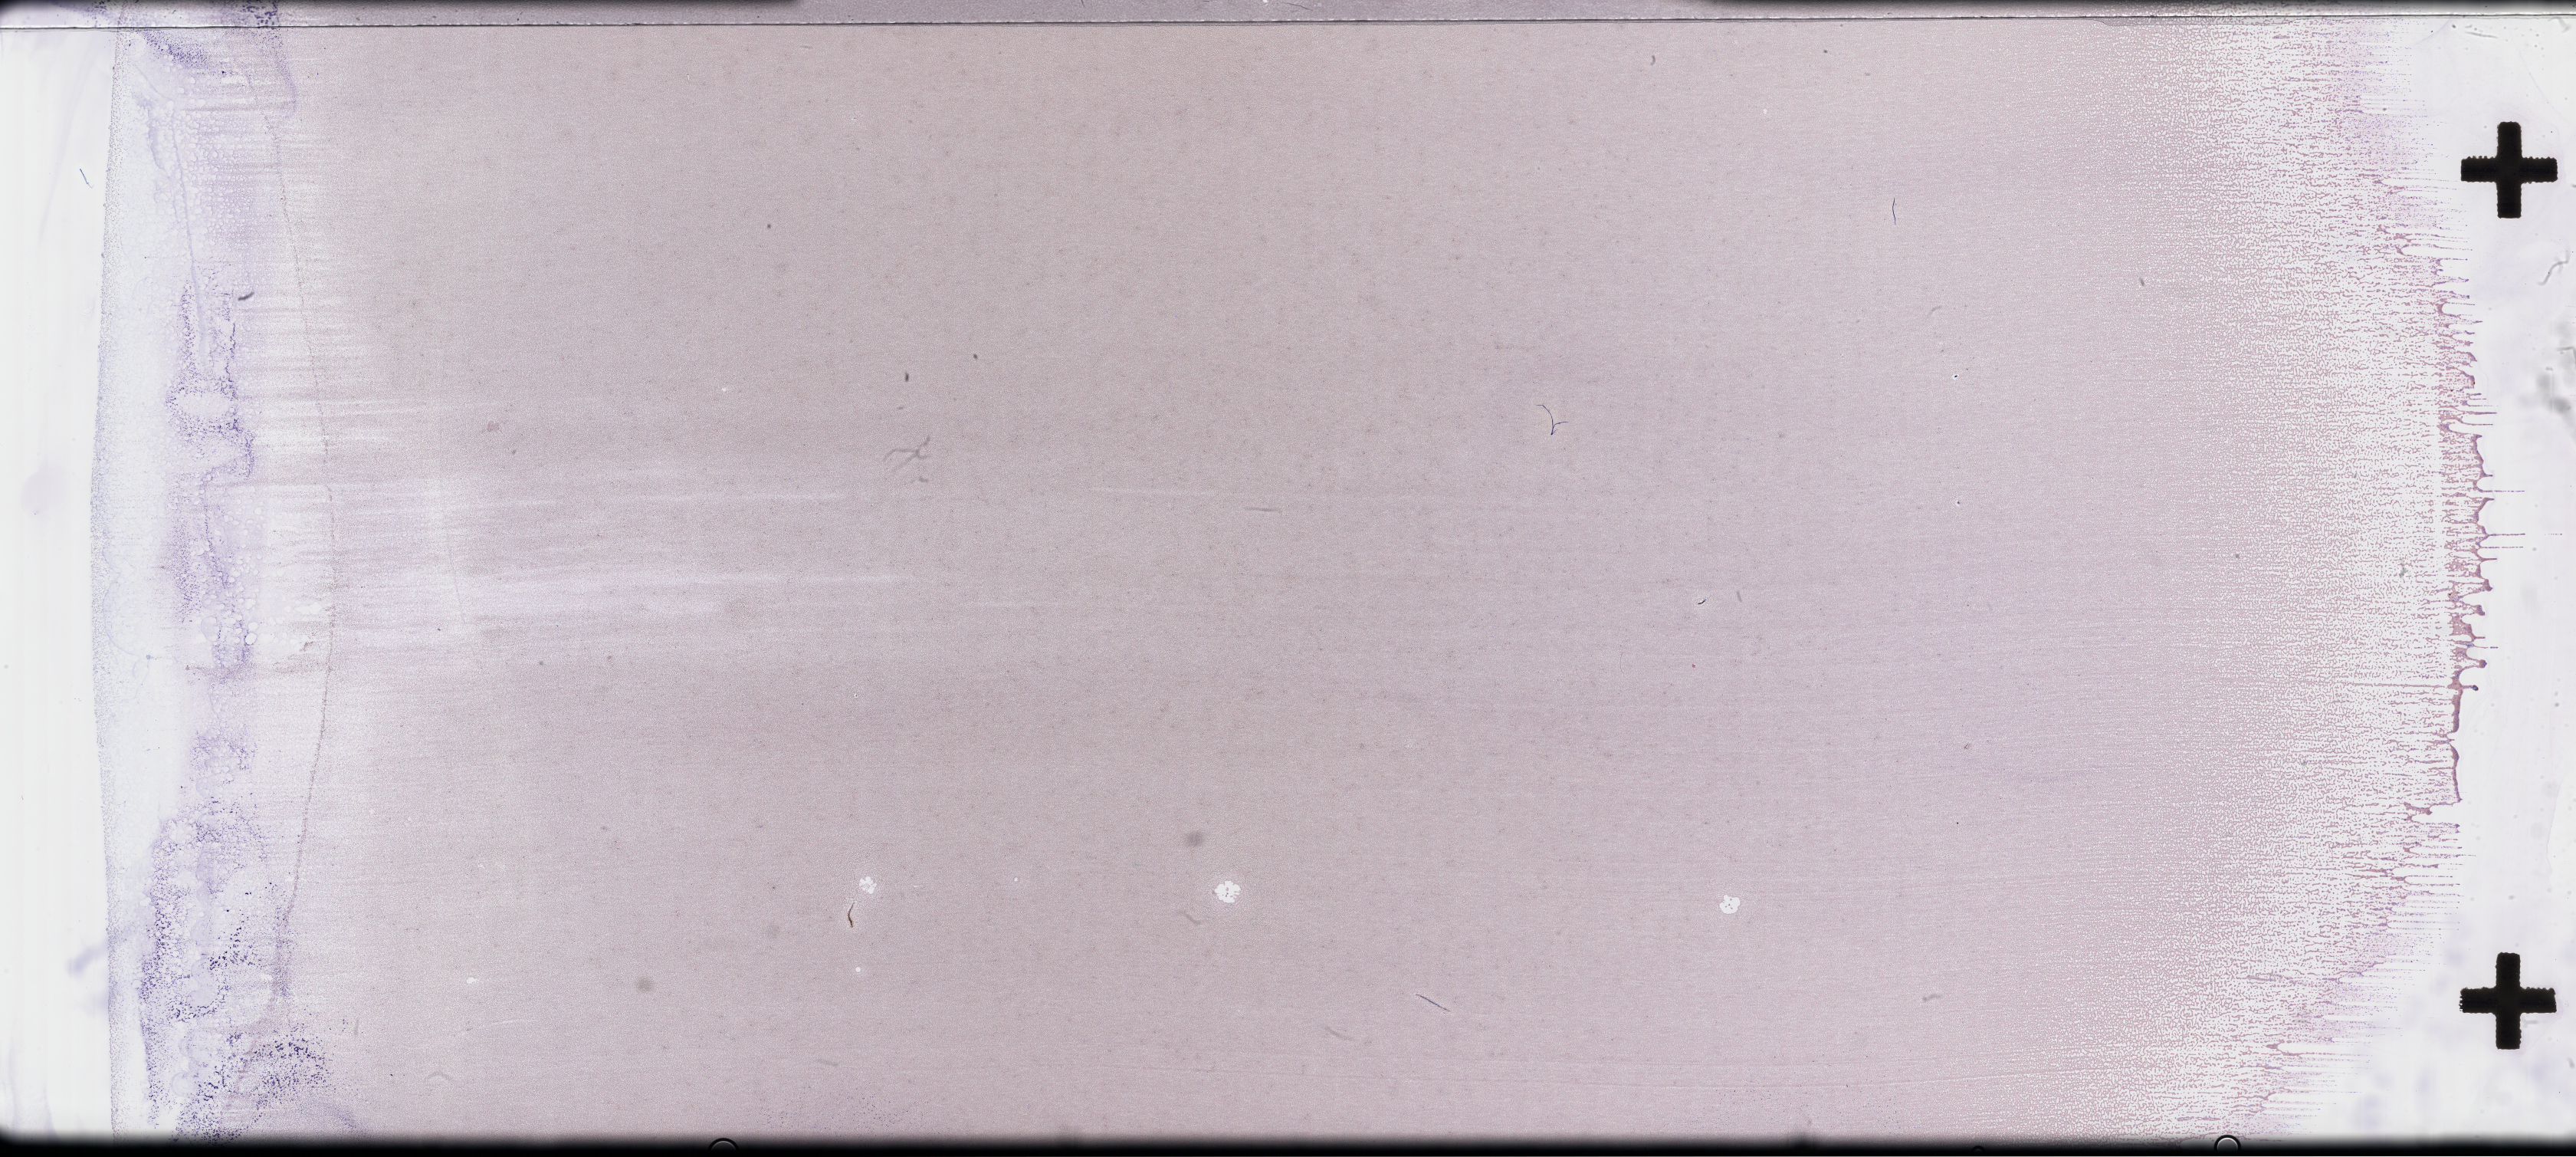
Whole-slide image of a whole blood smear, Wright-Giemsa stain, a low-resolution overview of the entire scanned area, about 54.3 x 24.4 mm, collected on treatment. Patient sex: male.
Patient diagnosis: Plasma Cell Myeloma.